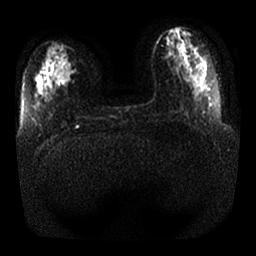
Breast MRI, one axial slice. Slice 9 of 25 in the series (ordered by position). Diffusion-weighted series; image 2 of 4 stored at this slice position (different b-values; order by instance number). 1.5 T. 4 mm slice thickness. 256 × 256 image matrix. Female patient.
Annotated regions visible in this slice (expert manual segmentation):
- tumour on diffusion-weighted imaging: bounding box <54,59,72,82> (left, top, right, bottom; pixels)